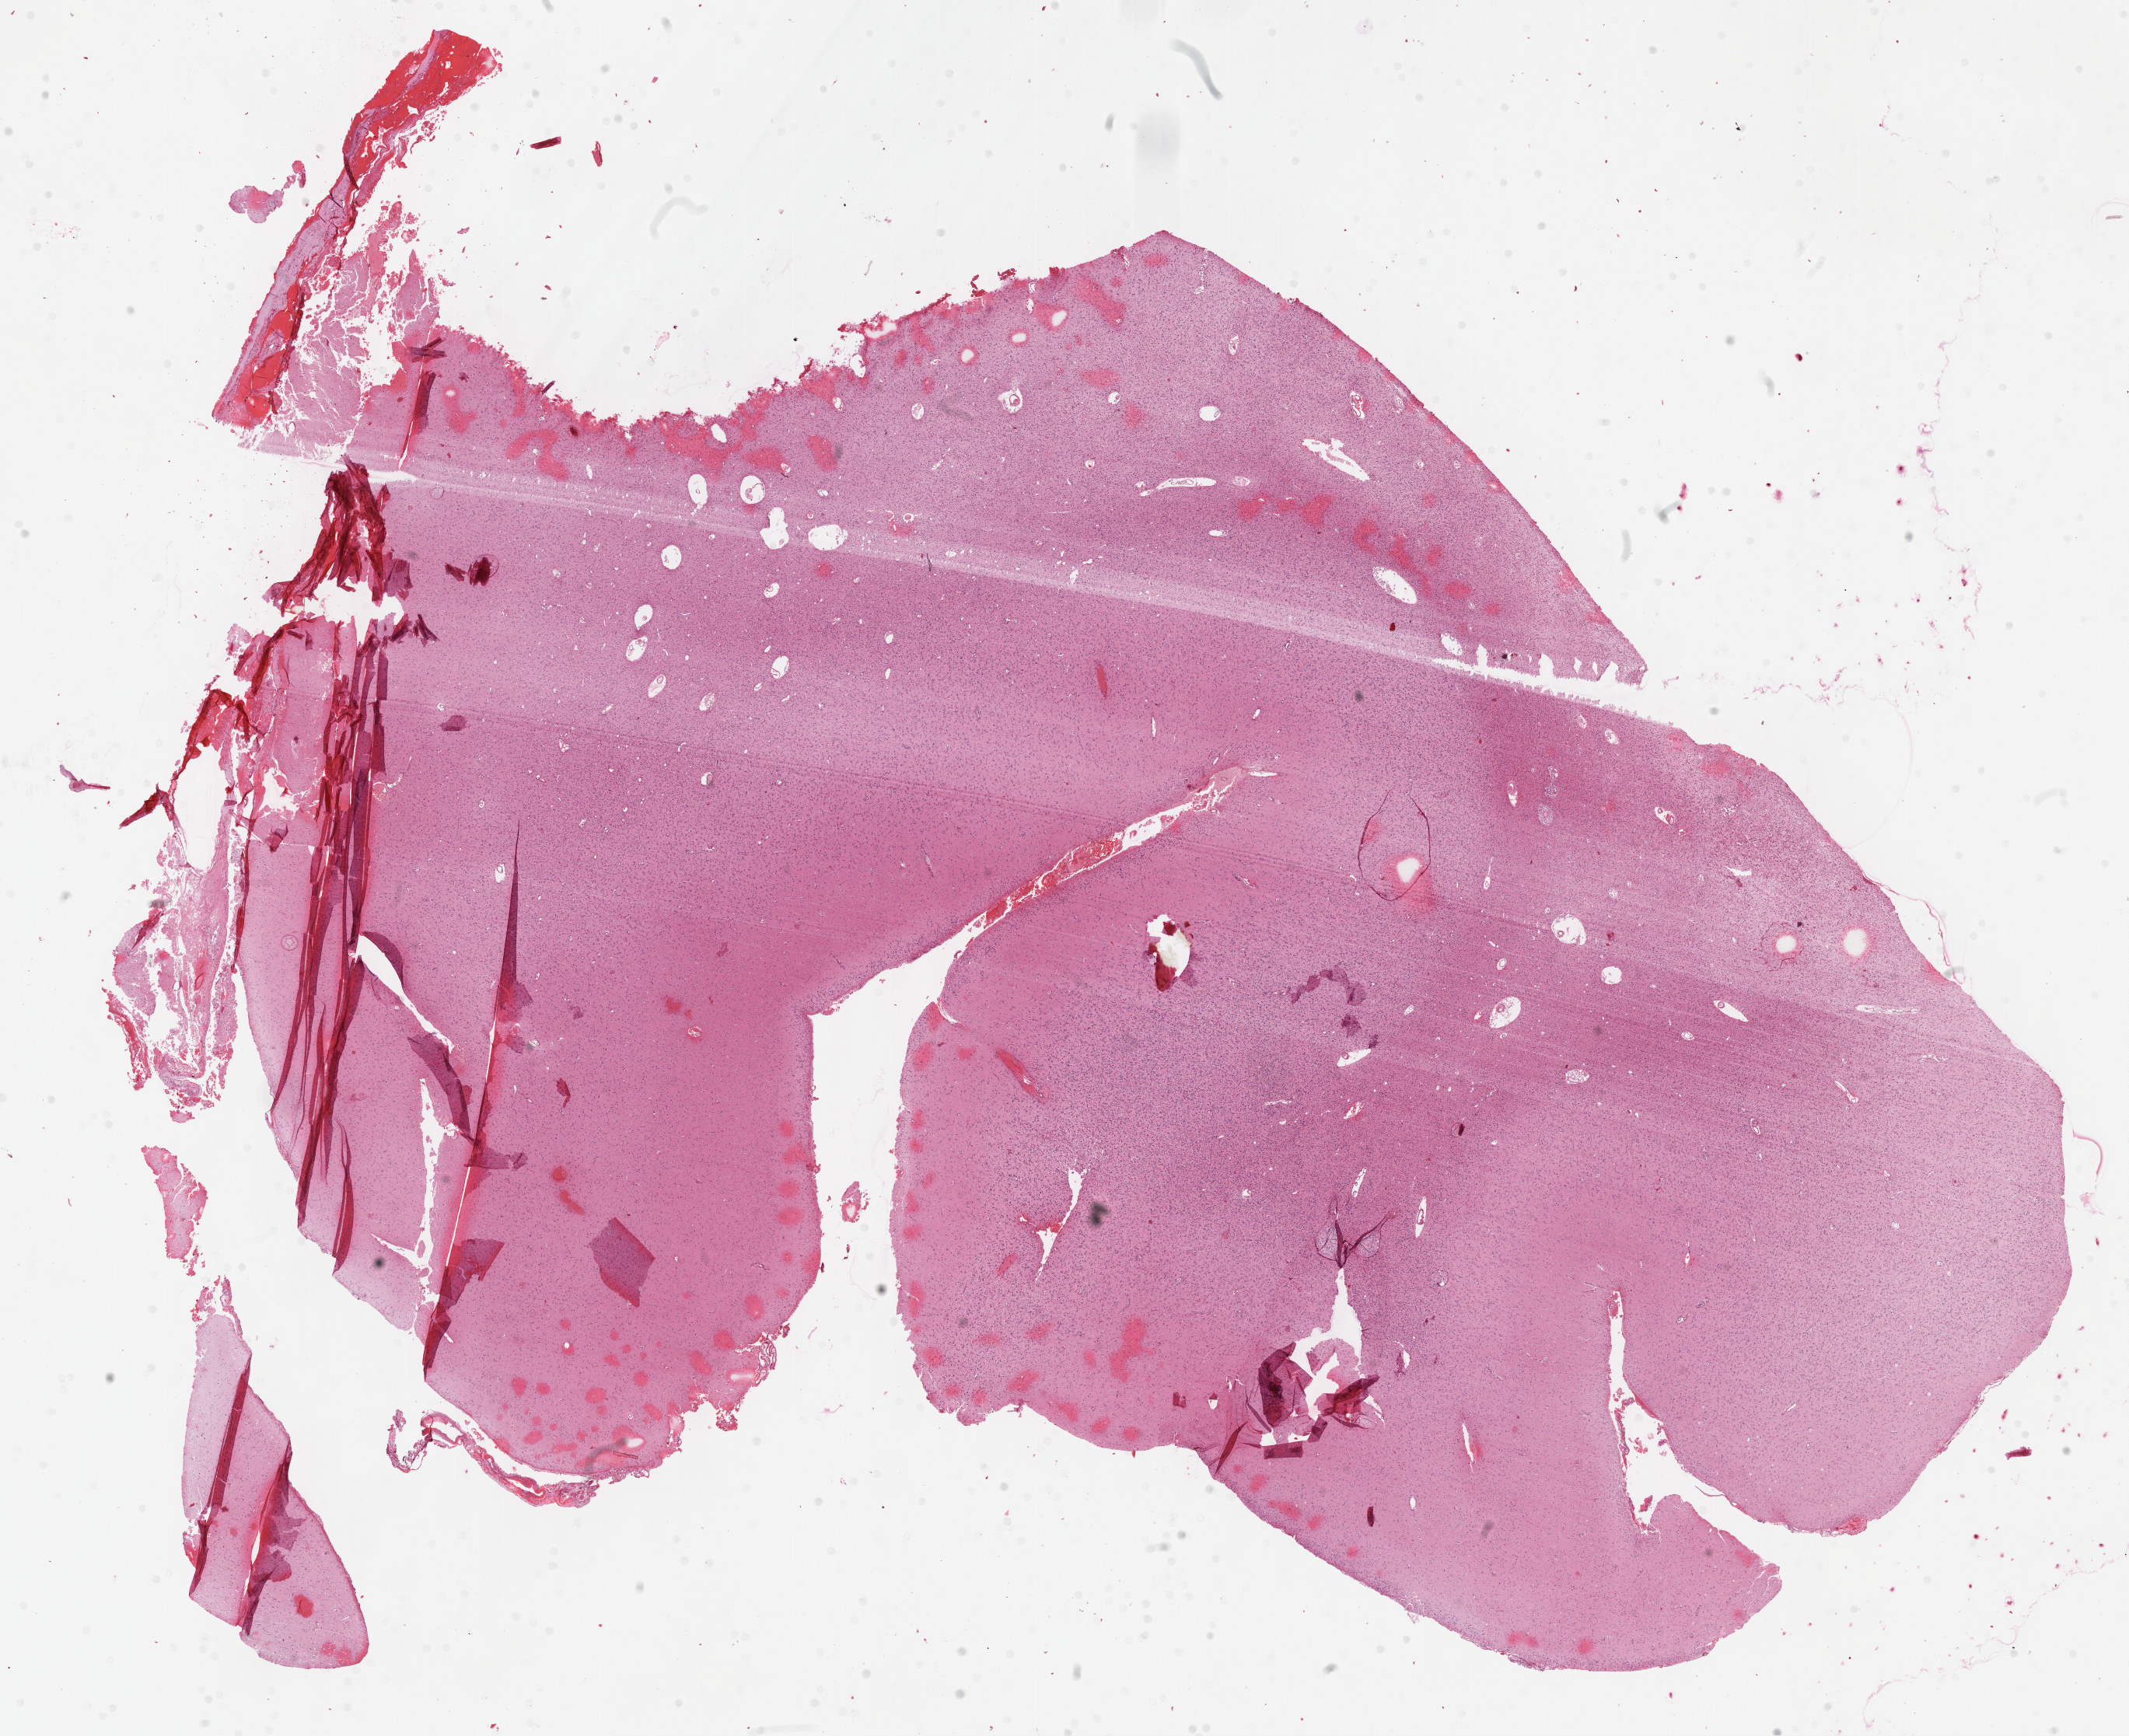
Hematoxylin and eosin (H&E) stained whole-slide image — whole scanned area (about 22.1 x 18.1 mm, acquisition: 40x scan) shown as a low-resolution overview, formalin-fixed paraffin-embedded (FFPE) diagnostic section, brain, primary tumour sample. Female patient; age at initial diagnosis 73 years.
Diagnosis: Oligodendroglioma, NOS (cerebrum).